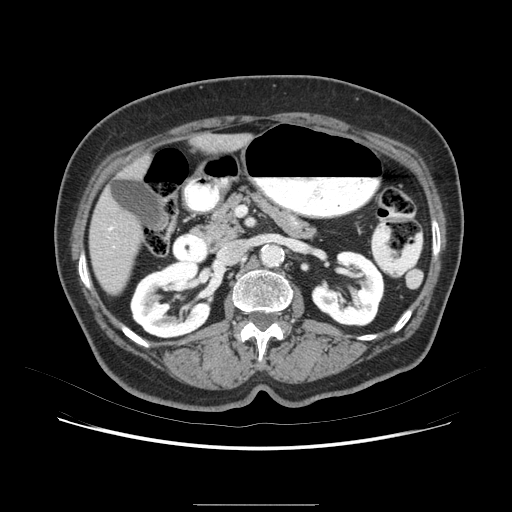
Contrast-enhanced abdominal CT (liver protocol), one axial slice; slice 29 of 79 in the series (ordered by position); 120 kVp; soft-tissue window (W 400 / L 40 HU); 2.5 mm slice thickness; 512 × 512 image matrix, field of view 380 × 380 mm. From the clinical record (not read from this slice): diagnosis: hepatocellular carcinoma (patient treated with transarterial chemoembolisation; whether this scan precedes or follows treatment is not stated here); TNM stage (as recorded): Stage-I.
Outlined on this slice (semi-automatically segmented with operator editing):
- liver parenchyma outside the tumour (the mass and vessels are separate outlines, so this box may not span the whole liver): bounding box <88,127,264,310> (left, top, right, bottom; pixels)
- liver vessels: <121,146,237,273>